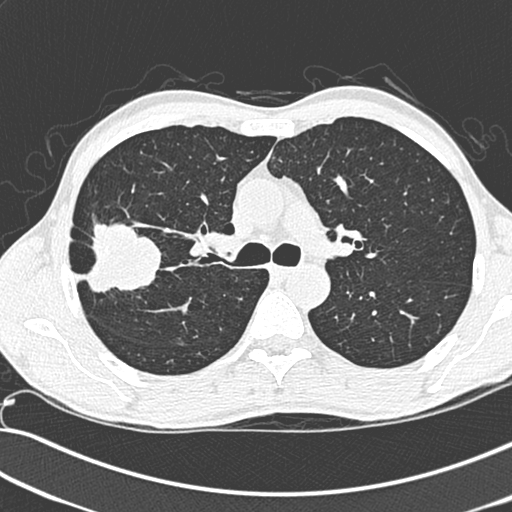
Low-dose screening chest CT, one axial slice; slice 197 of 281 in the series (ordered by position); 120 kVp; lung window (W 1500 / L -600 HU); 512 × 512 image matrix, field of view 341 × 341 mm.
Structures marked on this image (manually delineated by an expert):
- lesion 1 (tumor, upper lobe of right lung): bounding box [x1, y1, x2, y2] px = [79, 219, 166, 297]